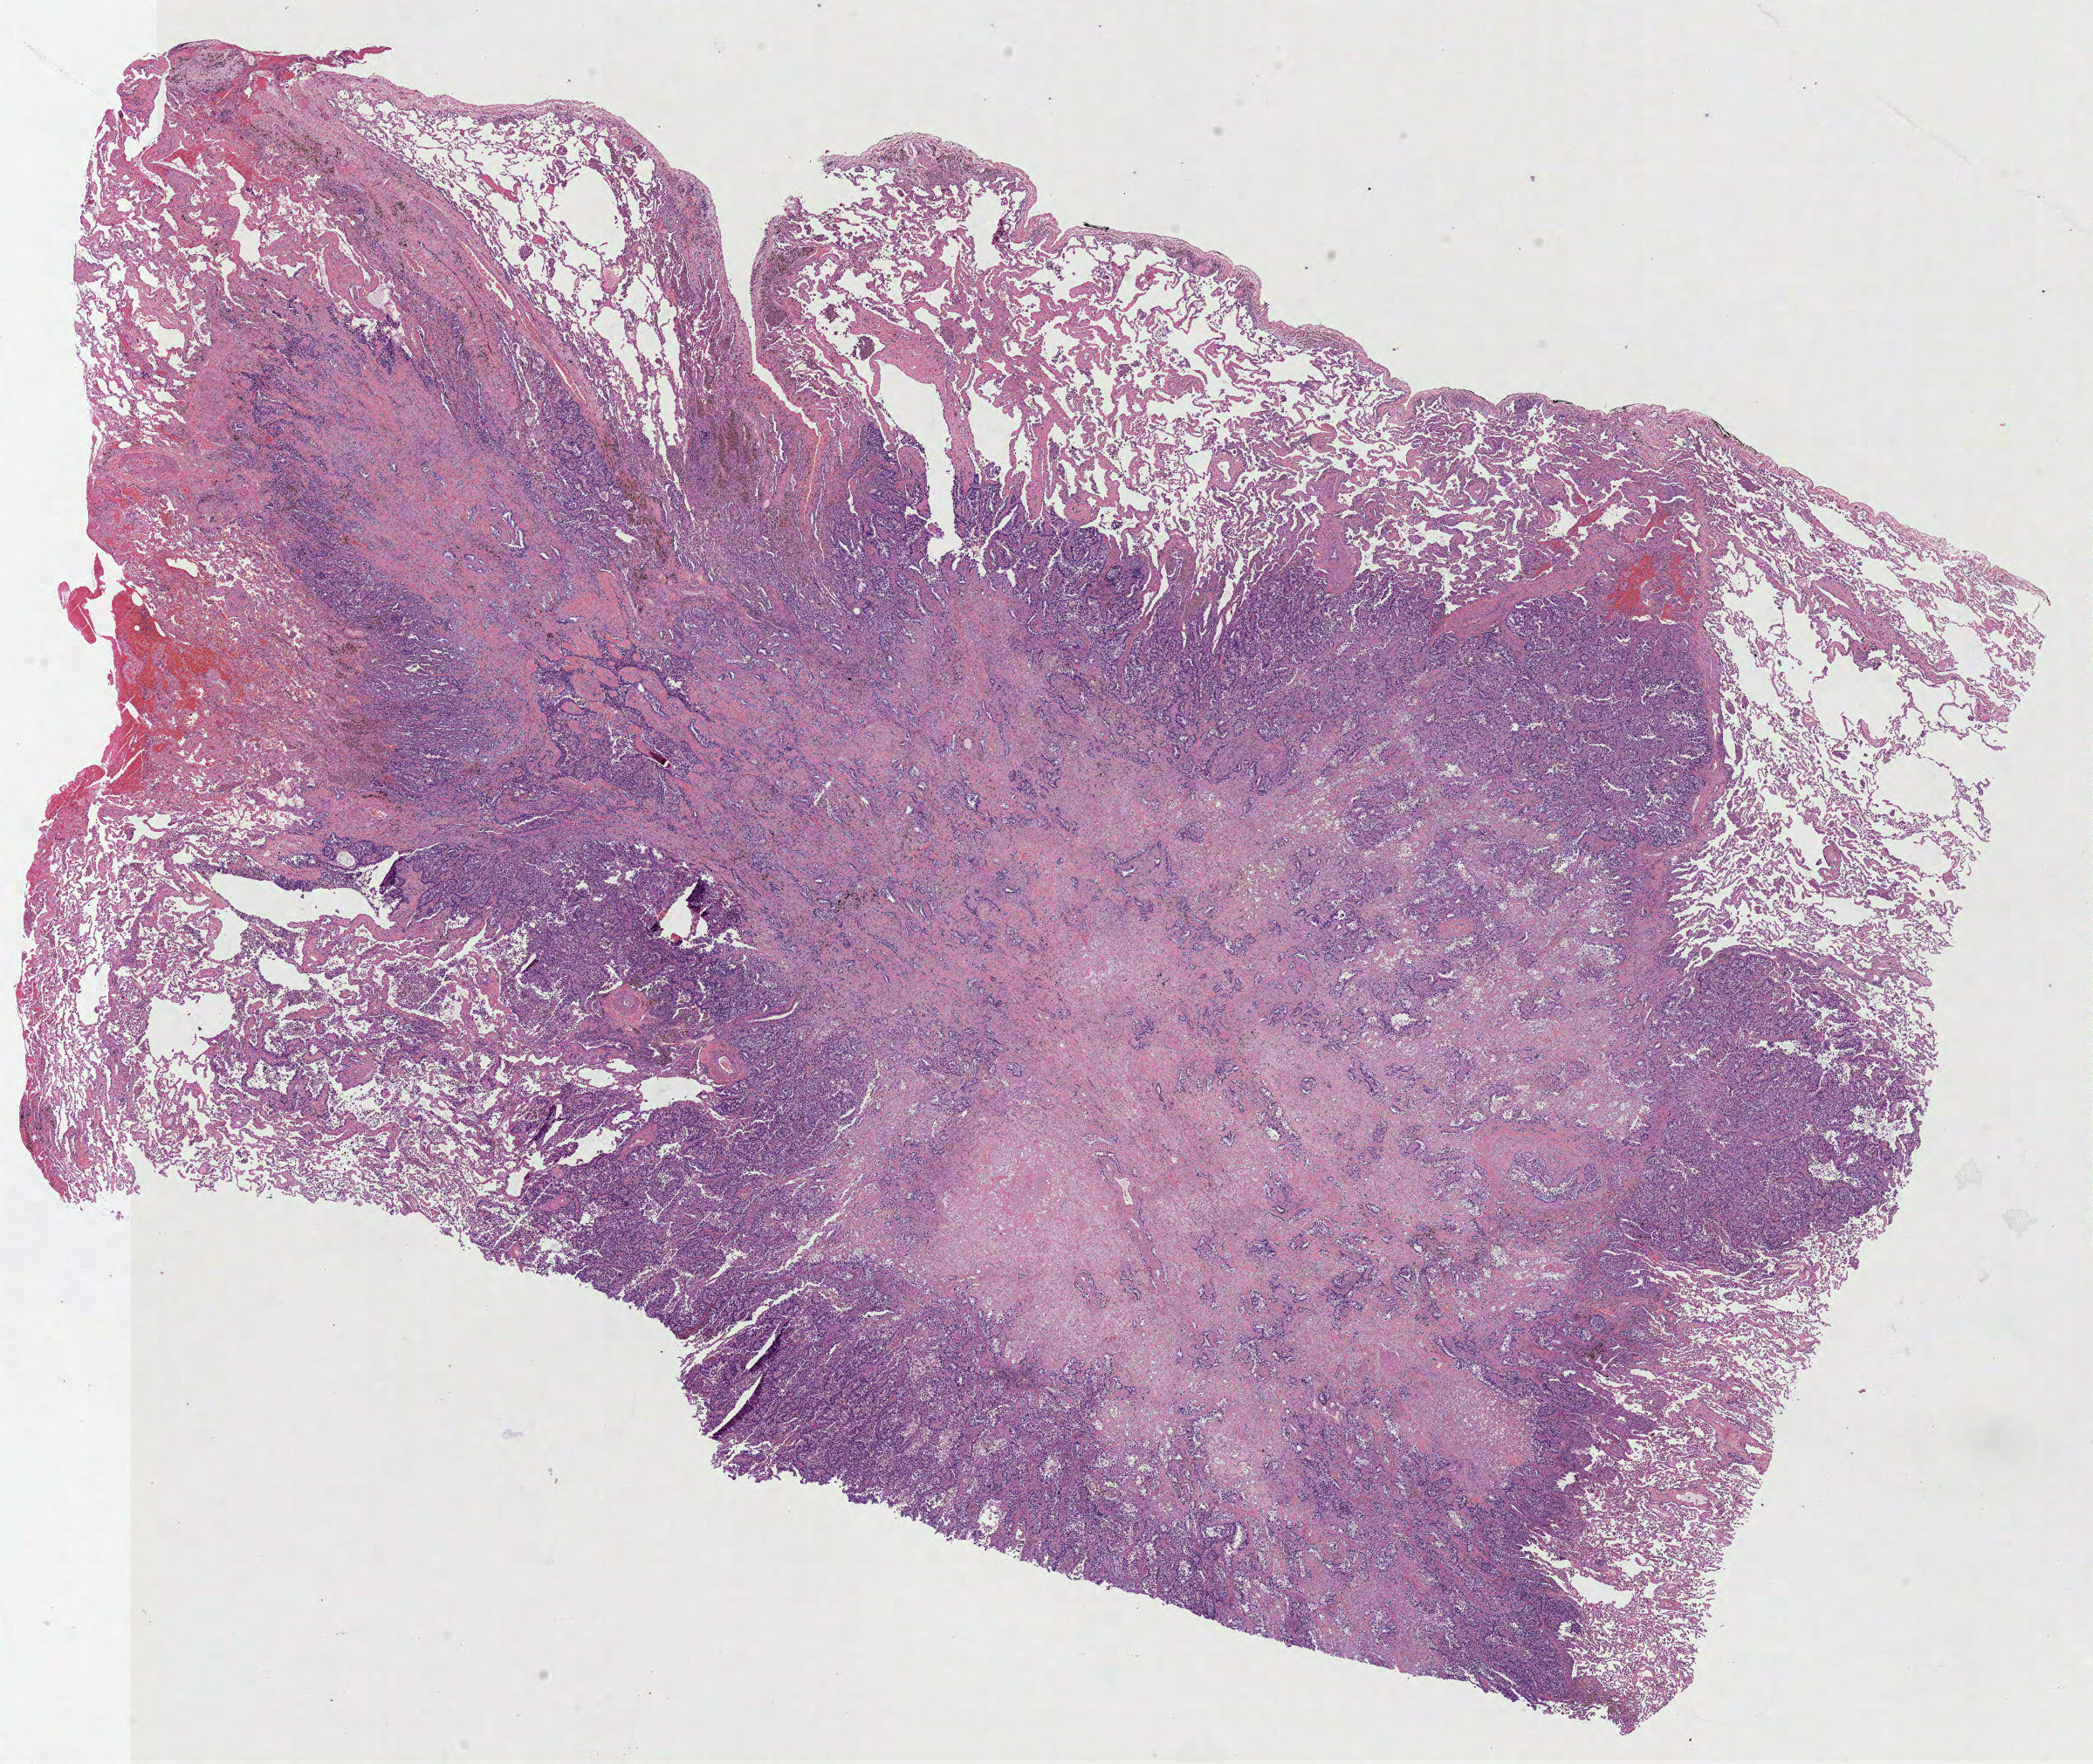
Digitized H&E tissue section (whole slide) — low-resolution overview of the scanned area, about 19.3 x 16.3 mm. FFPE section. Sample: primary tumour, lung. Male, age 53 years at initial diagnosis.
AJCC pathologic stage: IA (7th edition). Diagnosis: Adenocarcinoma, NOS (upper lobe, lung). Laterality: right.